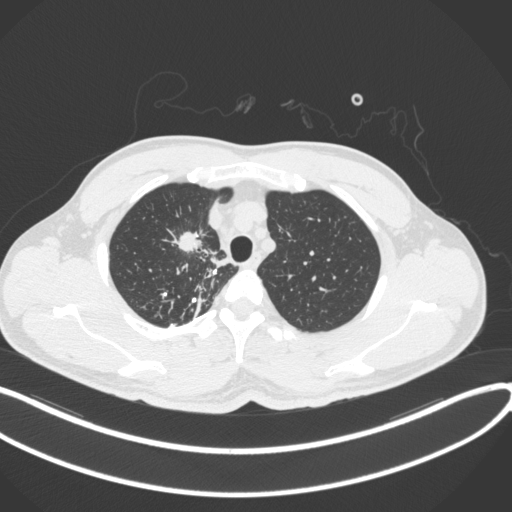
Chest CT, one axial slice; position 307 of 391 along the scan axis; reconstruction kernel B31f; 120 kVp; lung window (W 1500 / L -600 HU); 512 × 512 image matrix. Male patient, age 48 years. From the clinical record (not read from this slice): clinical TNM (as recorded): T1c N1 M1.
Structures marked on this image (rectangle marked by the reading radiologist):
- lung tumour (recorded histology: adenocarcinoma): bounding box (x1, y1, x2, y2) in pixels: (170, 226, 205, 255)